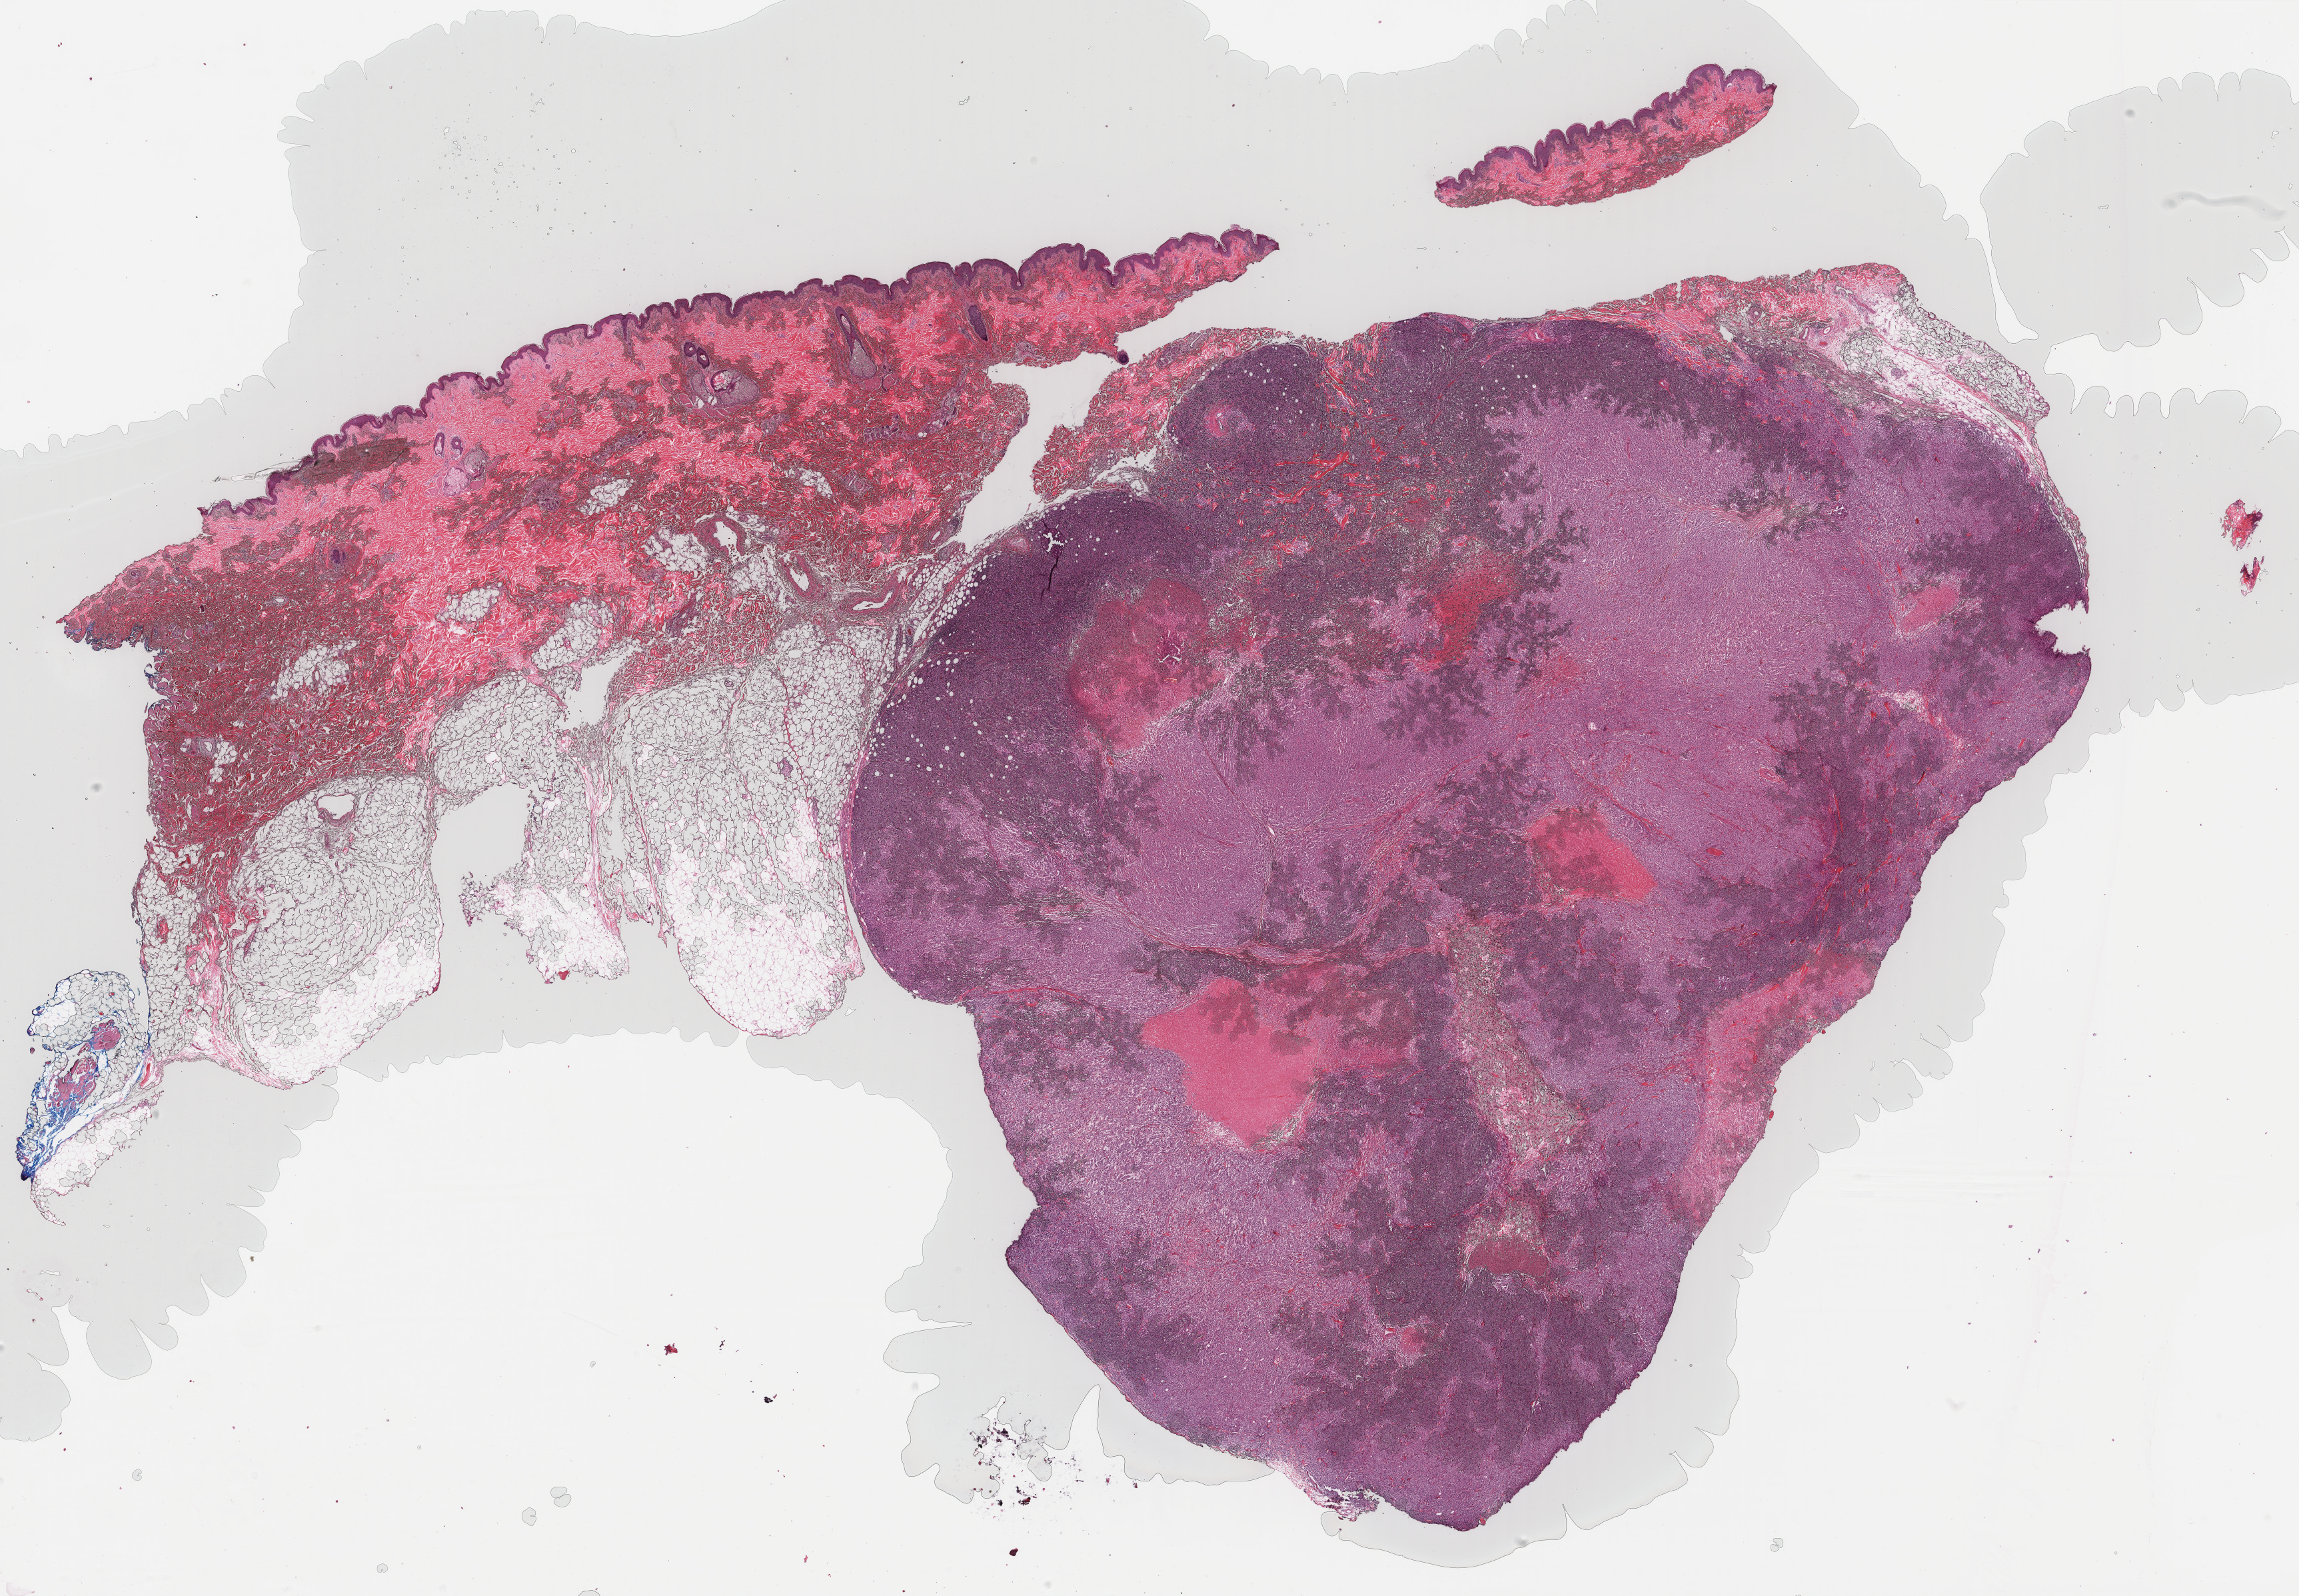
Hematoxylin and eosin (H&E) stained whole-slide image — whole scanned area (about 27.4 x 19.0 mm, slide scanned at 40x) shown as a low-resolution overview. Formalin-fixed paraffin-embedded (FFPE) diagnostic section. Skin, primary tumour sample. Patient: male, age at initial diagnosis 45 years.
Diagnosis: Malignant melanoma, NOS.